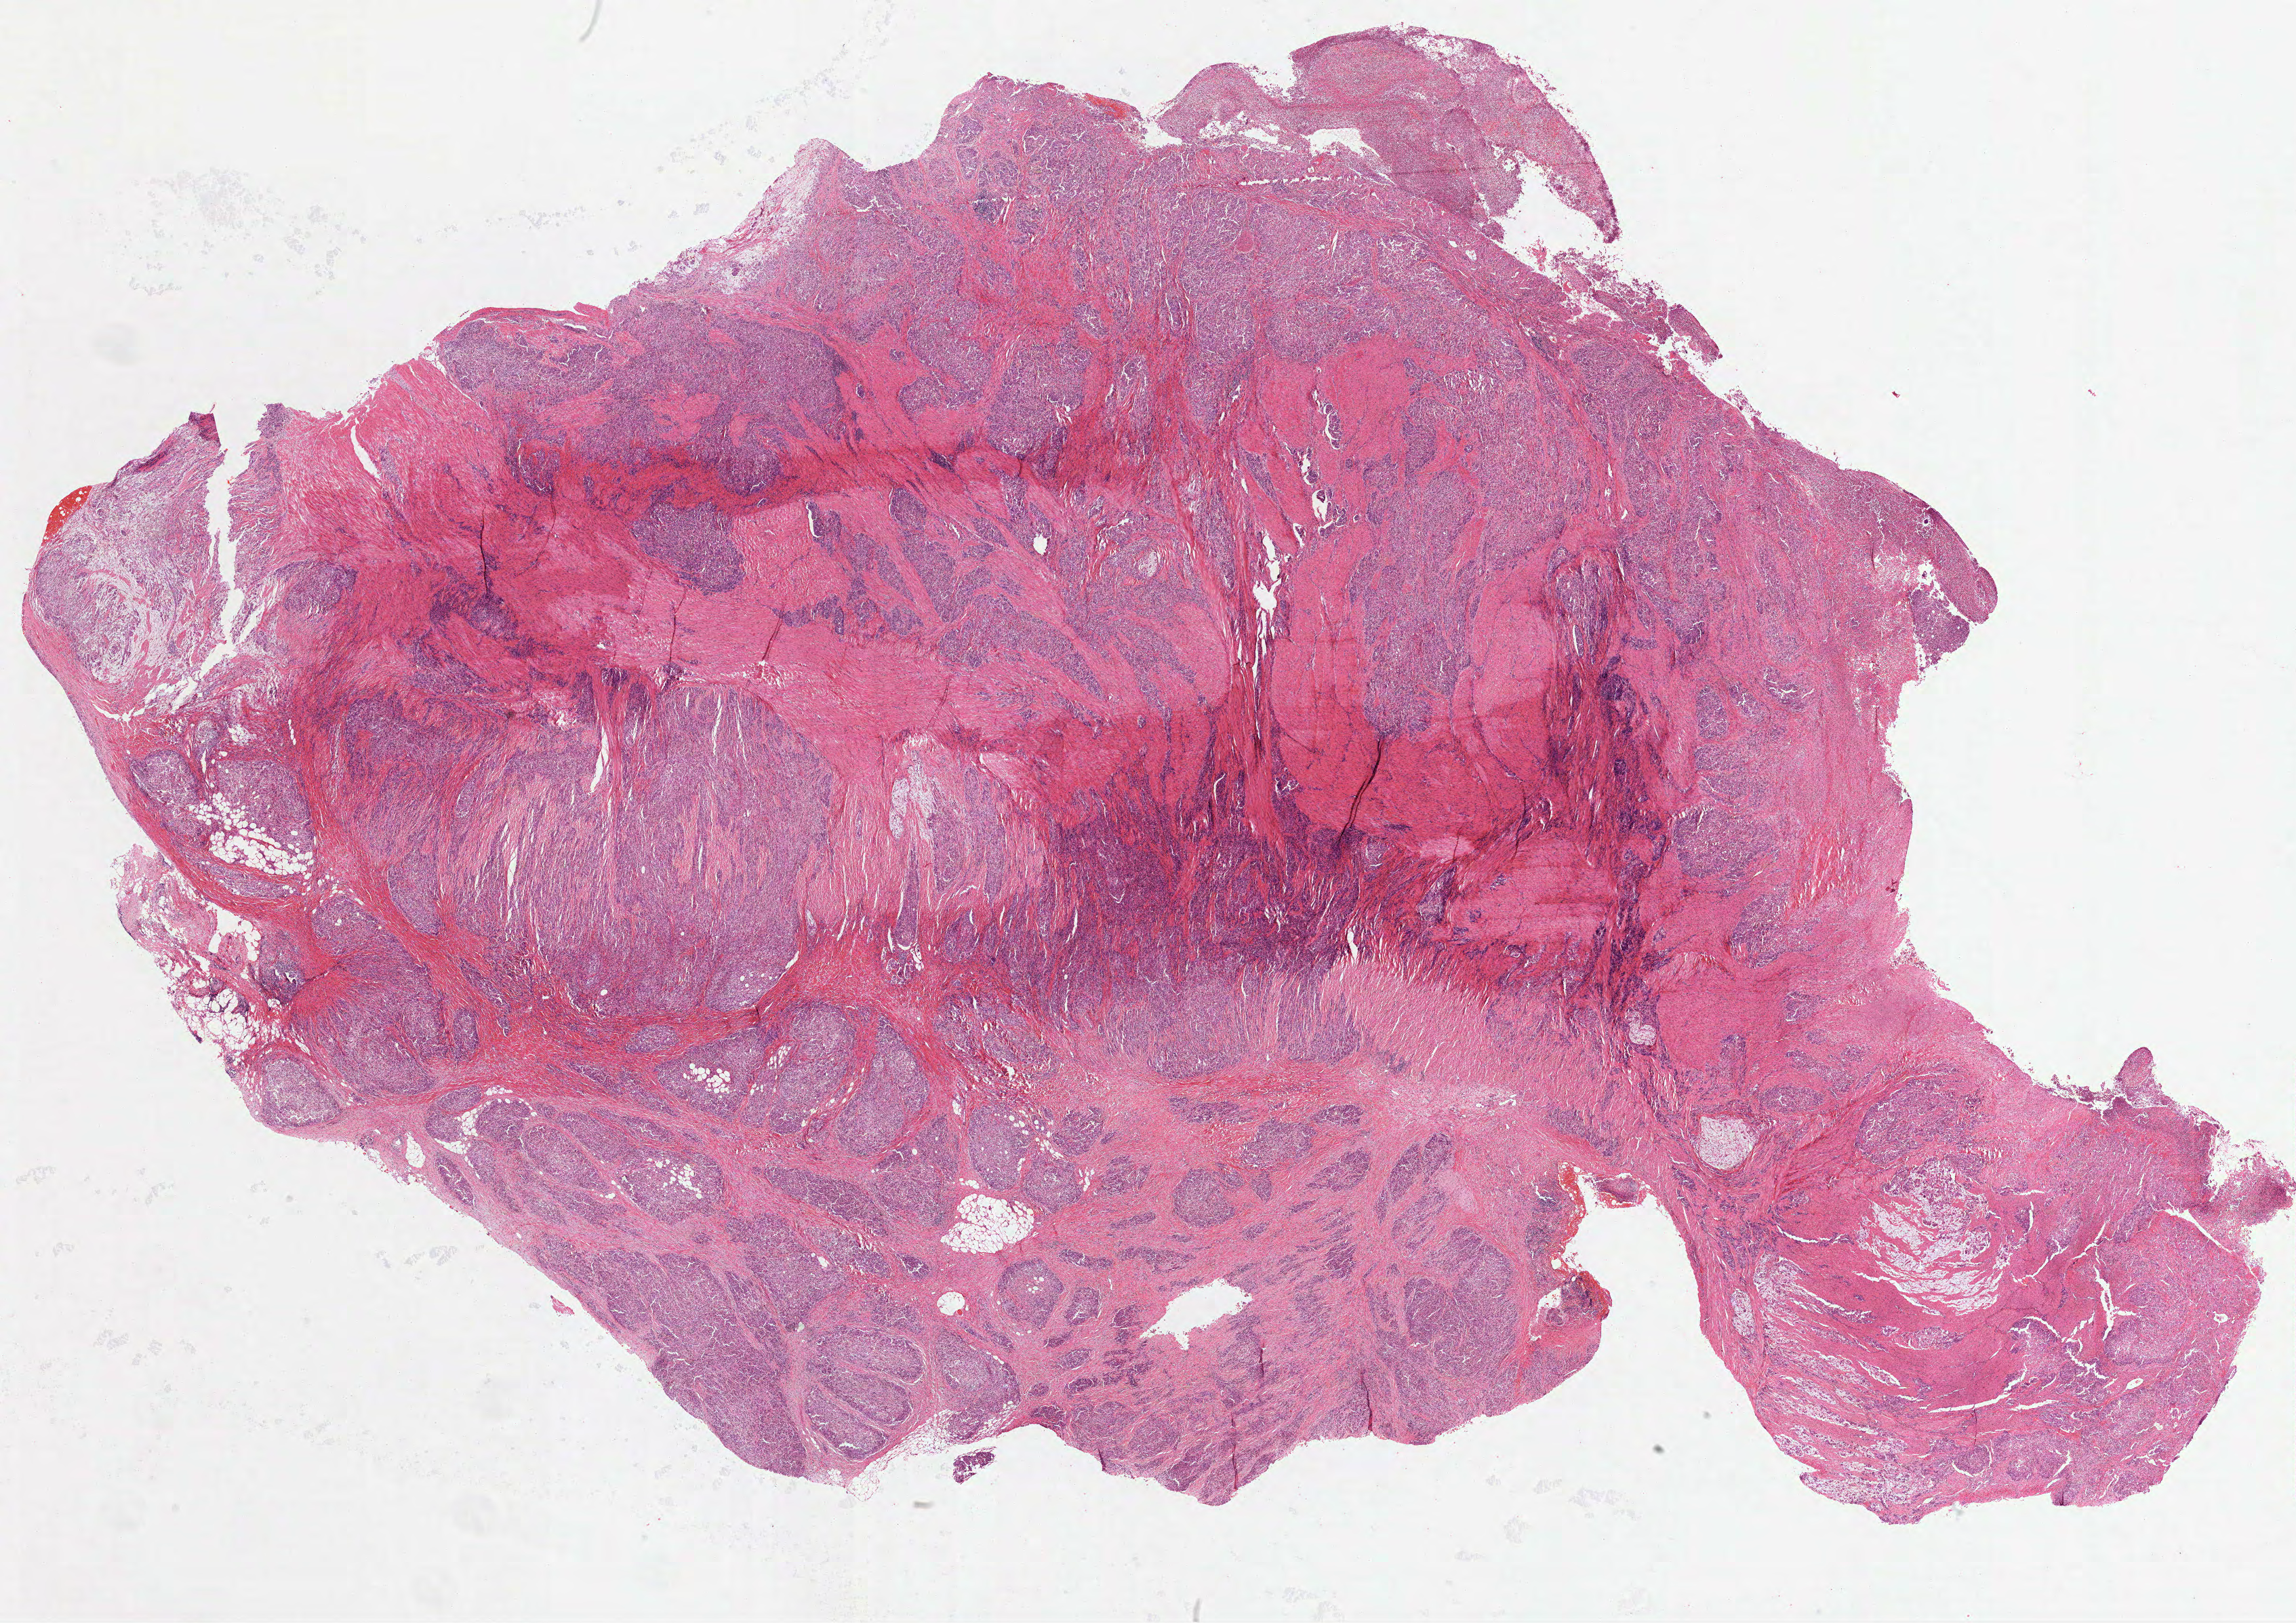
Digitized H&E-stained tissue section (whole slide) — shown as a low-resolution overview of the whole scanned area (about 27.3 x 19.3 mm). Formalin-fixed paraffin-embedded (FFPE) diagnostic section. Stomach, primary tumour sample. Male patient; age at initial diagnosis 65 years. Histologic grade: G3 (poorly differentiated).
- AJCC pathologic stage: IIIC (7th edition)
- histologic diagnosis: Adenocarcinoma, NOS (fundus of stomach)
- lymph nodes positive (case pathology): 15 of 30 examined